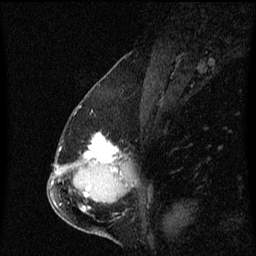
Breast MRI (dynamic contrast-enhanced), one sagittal slice. Position 32 of 60 along the scan axis. Dynamic contrast-enhanced series, image 2 of 3 at this slice position (ordered by acquisition). 1.5 T. TE 4.2 ms, TR 8.4 ms. 256 × 256 image matrix, field of view 200 × 200 mm. Female patient, age 57 years. Case-level facts recorded for this patient, not image findings: setting: breast cancer imaged before/during neoadjuvant chemotherapy; receptor status: HR-positive, HER2-negative.
Outlined on this slice (semi-automatically segmented with operator editing):
- analysis volume of interest (the breast-tissue region the enhancement analysis was run in; not a lesion): box from (x=66, y=118) to (x=129, y=177) px
- tumour enhancement mask (voxels above the 70 % enhancement threshold inside the analysis volume of interest): (x=84, y=134)–(x=122, y=177)